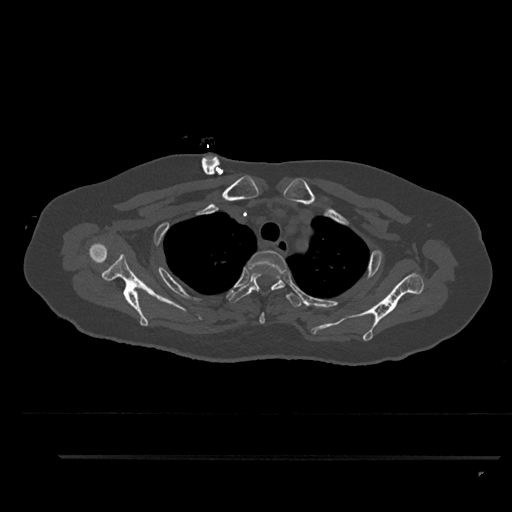
CT including the spine, one axial slice. Slice 700 of 797 in the series (ordered by position). 120 kVp. Bone window (W 1800 / L 400 HU). 0.5 mm slice thickness. 512 × 512 image matrix. Female patient, age 44 years. From the clinical record (not read from this slice): primary cancer: renal.
Structures marked on this image (semi-automatically segmented with operator editing):
- T2 vertebra: bounding box (x1, y1, x2, y2) in pixels: (247, 250, 287, 324)
- T3 vertebra: (228, 272, 304, 307)